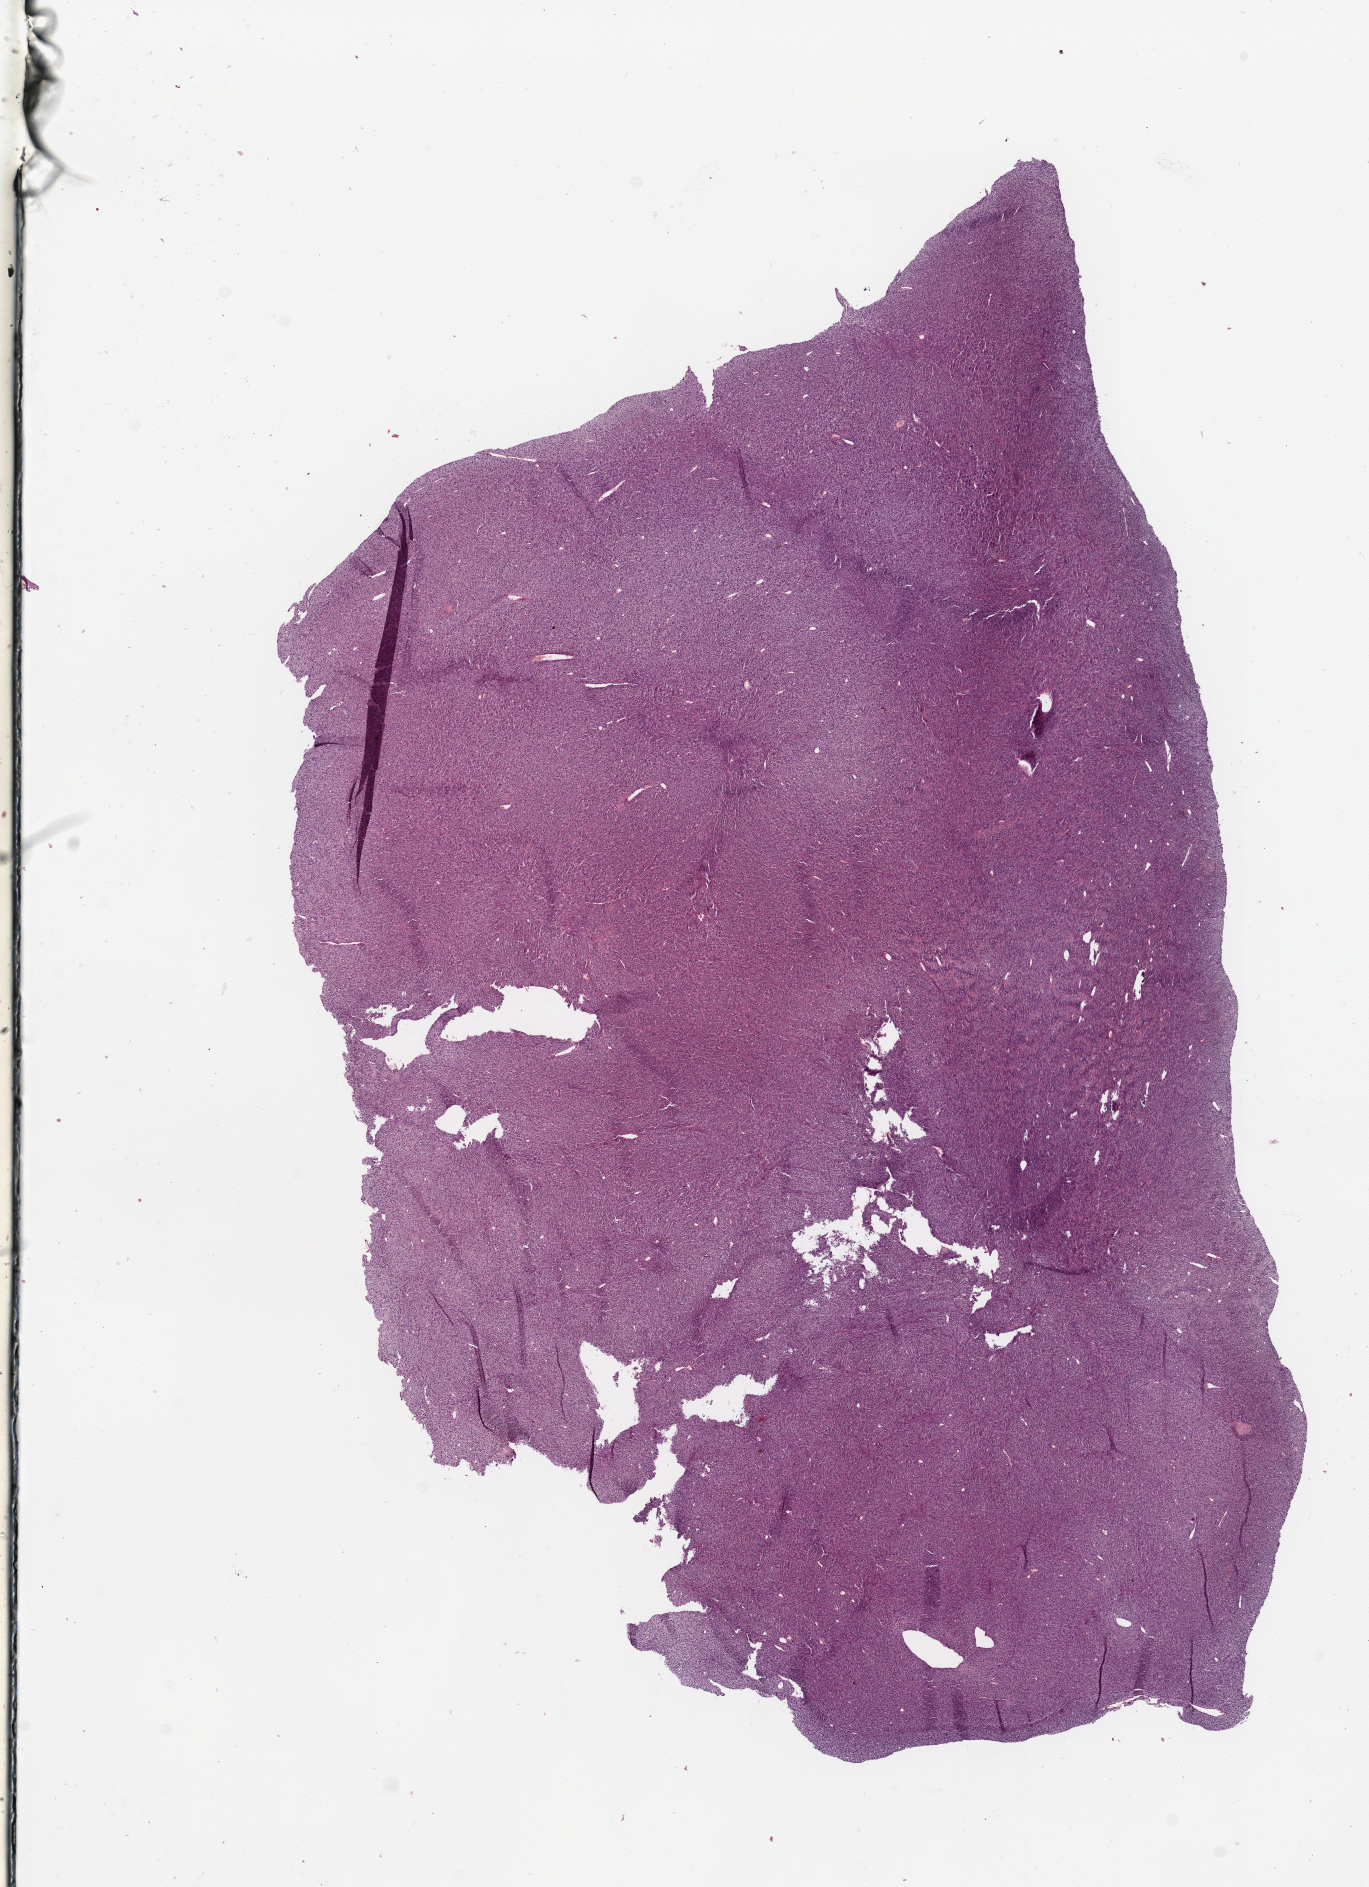
Whole-slide histology image, H&E-stained, a low-resolution overview of the entire scanned area, about 10.8 x 14.9 mm (from a 20x scan), tumour tissue sample. Female, 43 y/o.
Primary tumour site (as recorded): lower extremity. Patient diagnosis (cohort enrolment): sarcoma (site not recorded at cohort level).